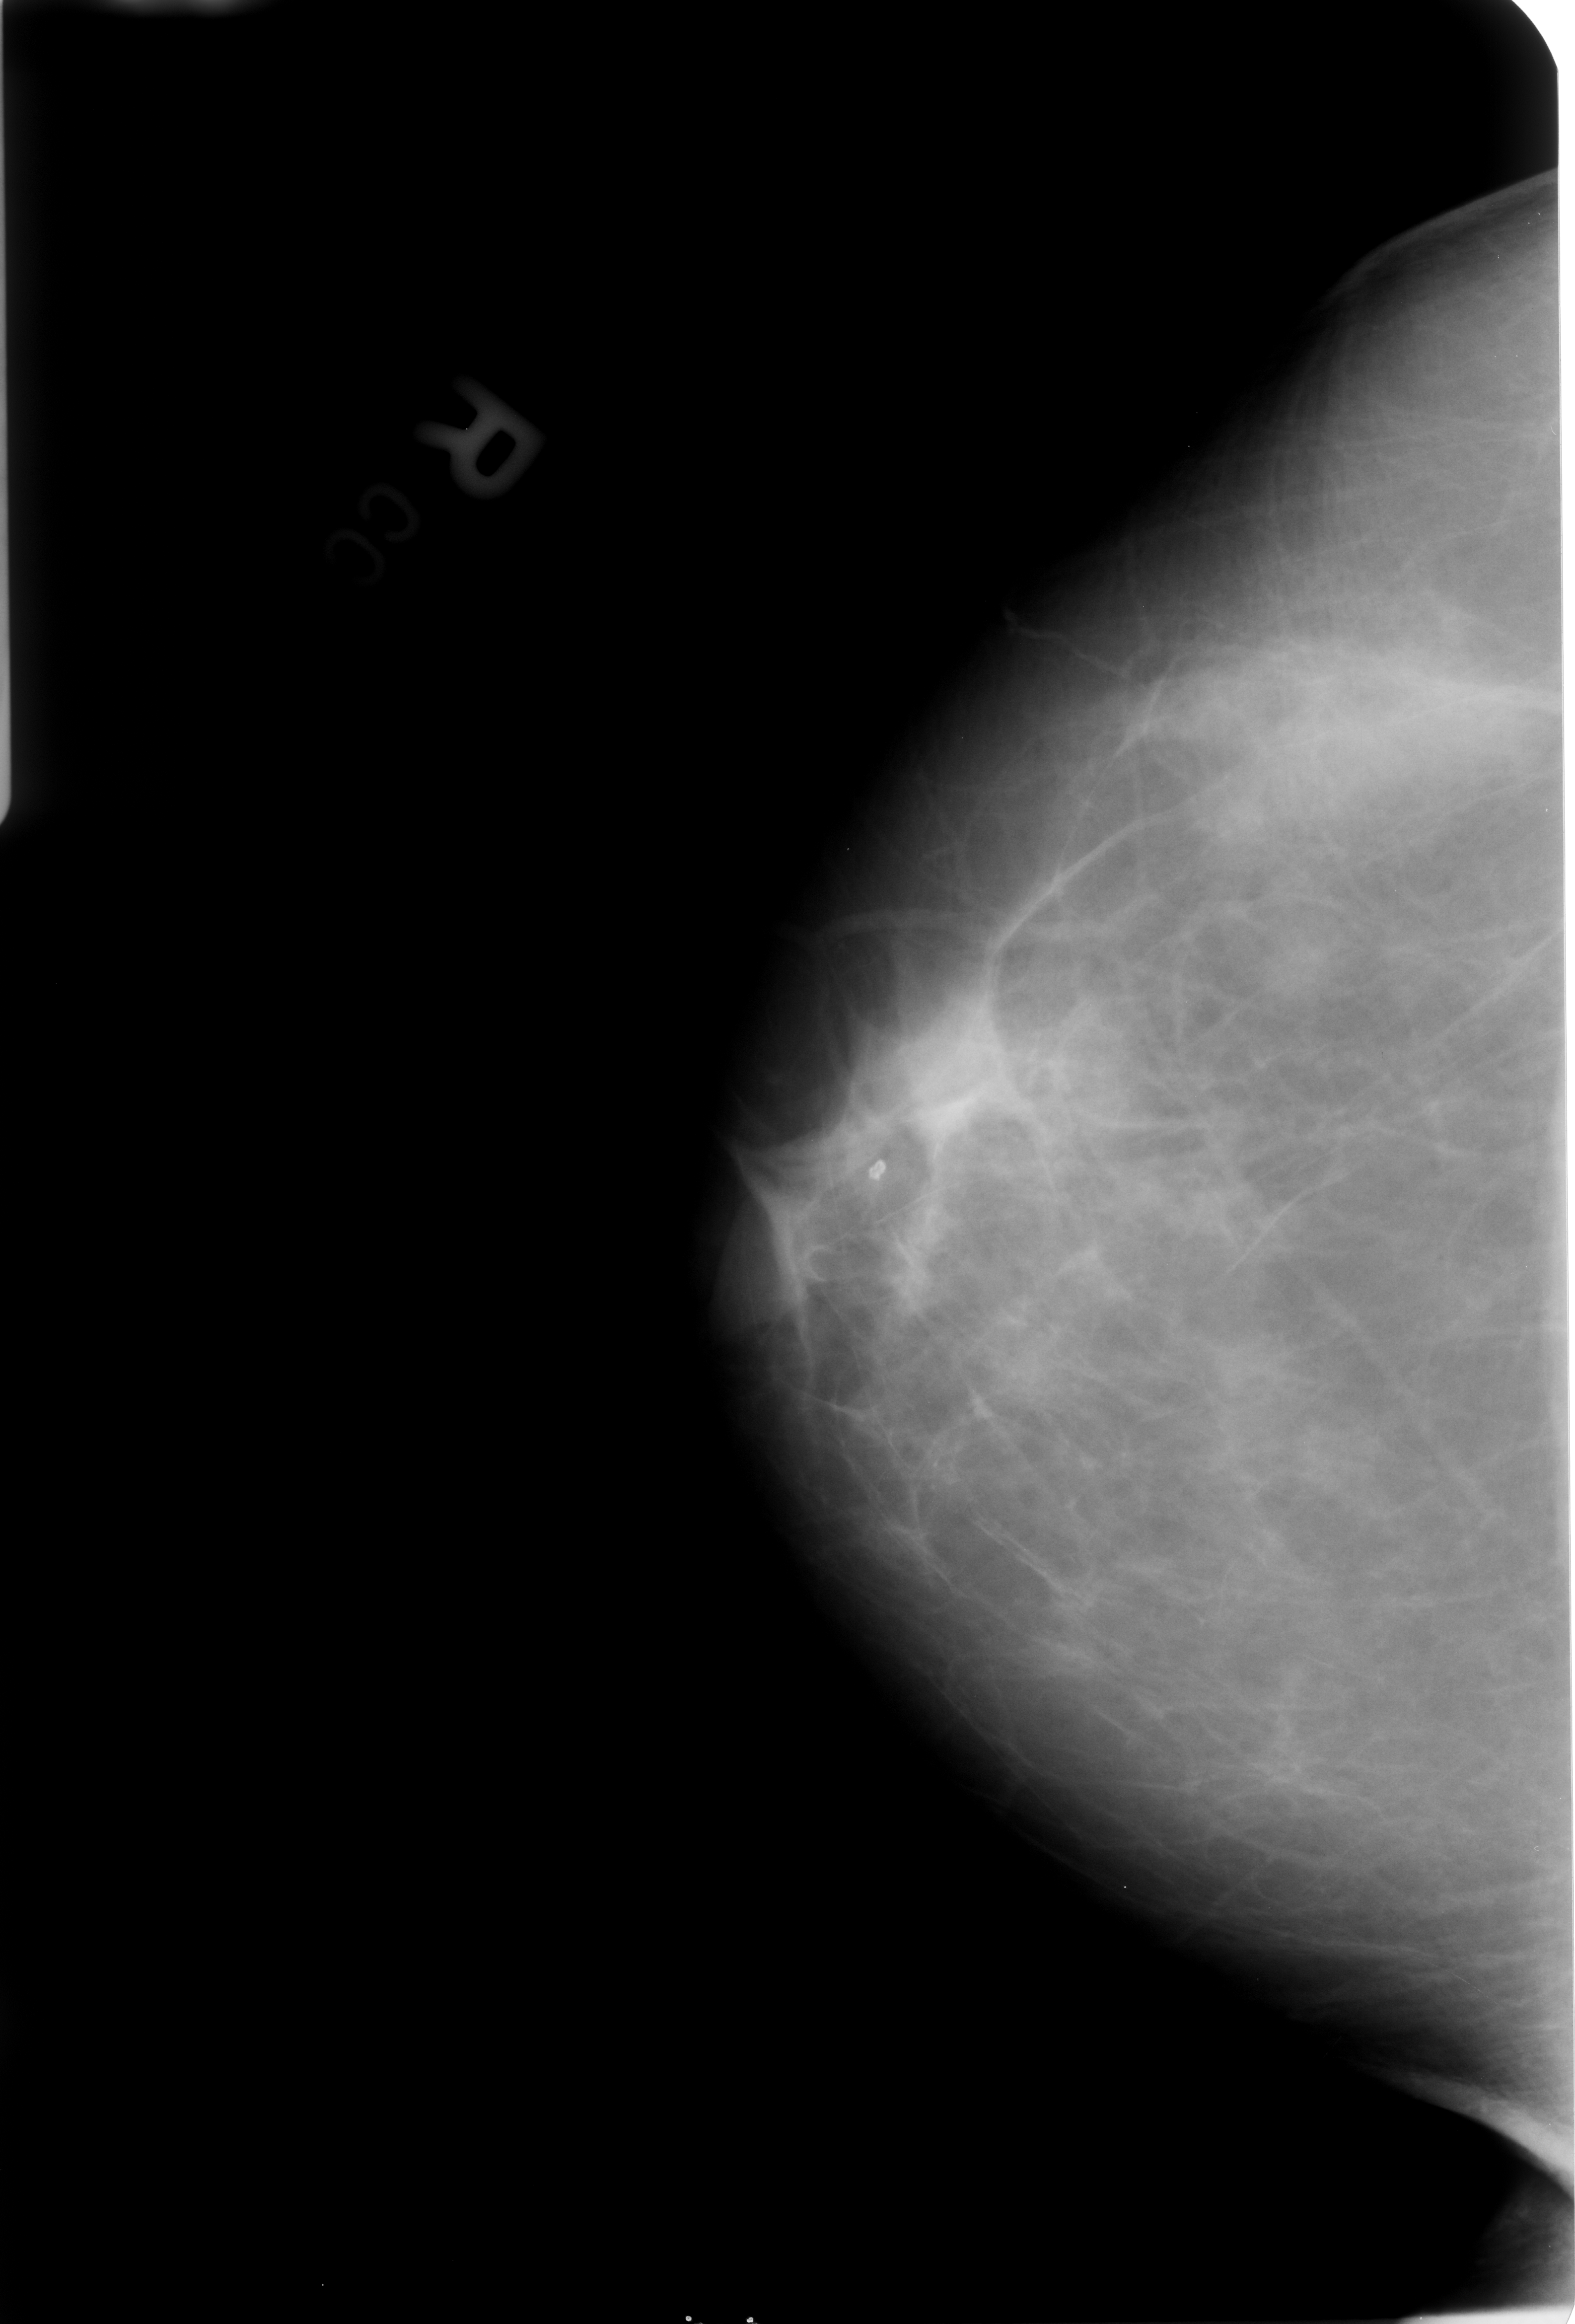
Mammogram (digitized film), right breast, craniocaudal (CC) view, BI-RADS breast density category 2 (scale 1–4).
- Radiologist-marked abnormalities on this image: calcifications, morphology lucent center; BI-RADS assessment category 2; benign without callback (not worked up further).